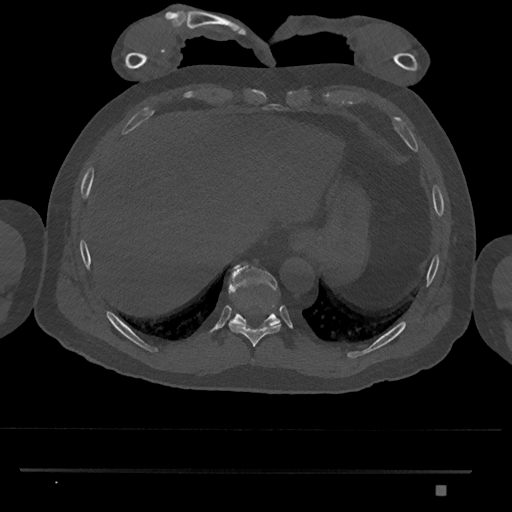
CT including the spine, one axial slice. Slice 1035 of 1134 in the series (ordered by position). Reconstruction kernel Br40s/3. 120 kVp. Bone window (W 1800 / L 400 HU). 0.5 mm slice thickness. 512 × 512 image matrix, field of view 429 × 429 mm. Patient: male, 65 years. From the clinical record (not read from this slice): primary cancer: prostate.
Outlined on this slice (semi-automatically segmented with operator editing):
- T10 vertebra: bounding box (x1, y1, x2, y2) in pixels: (228, 264, 281, 328)
- T9 vertebra: (229, 302, 281, 347)